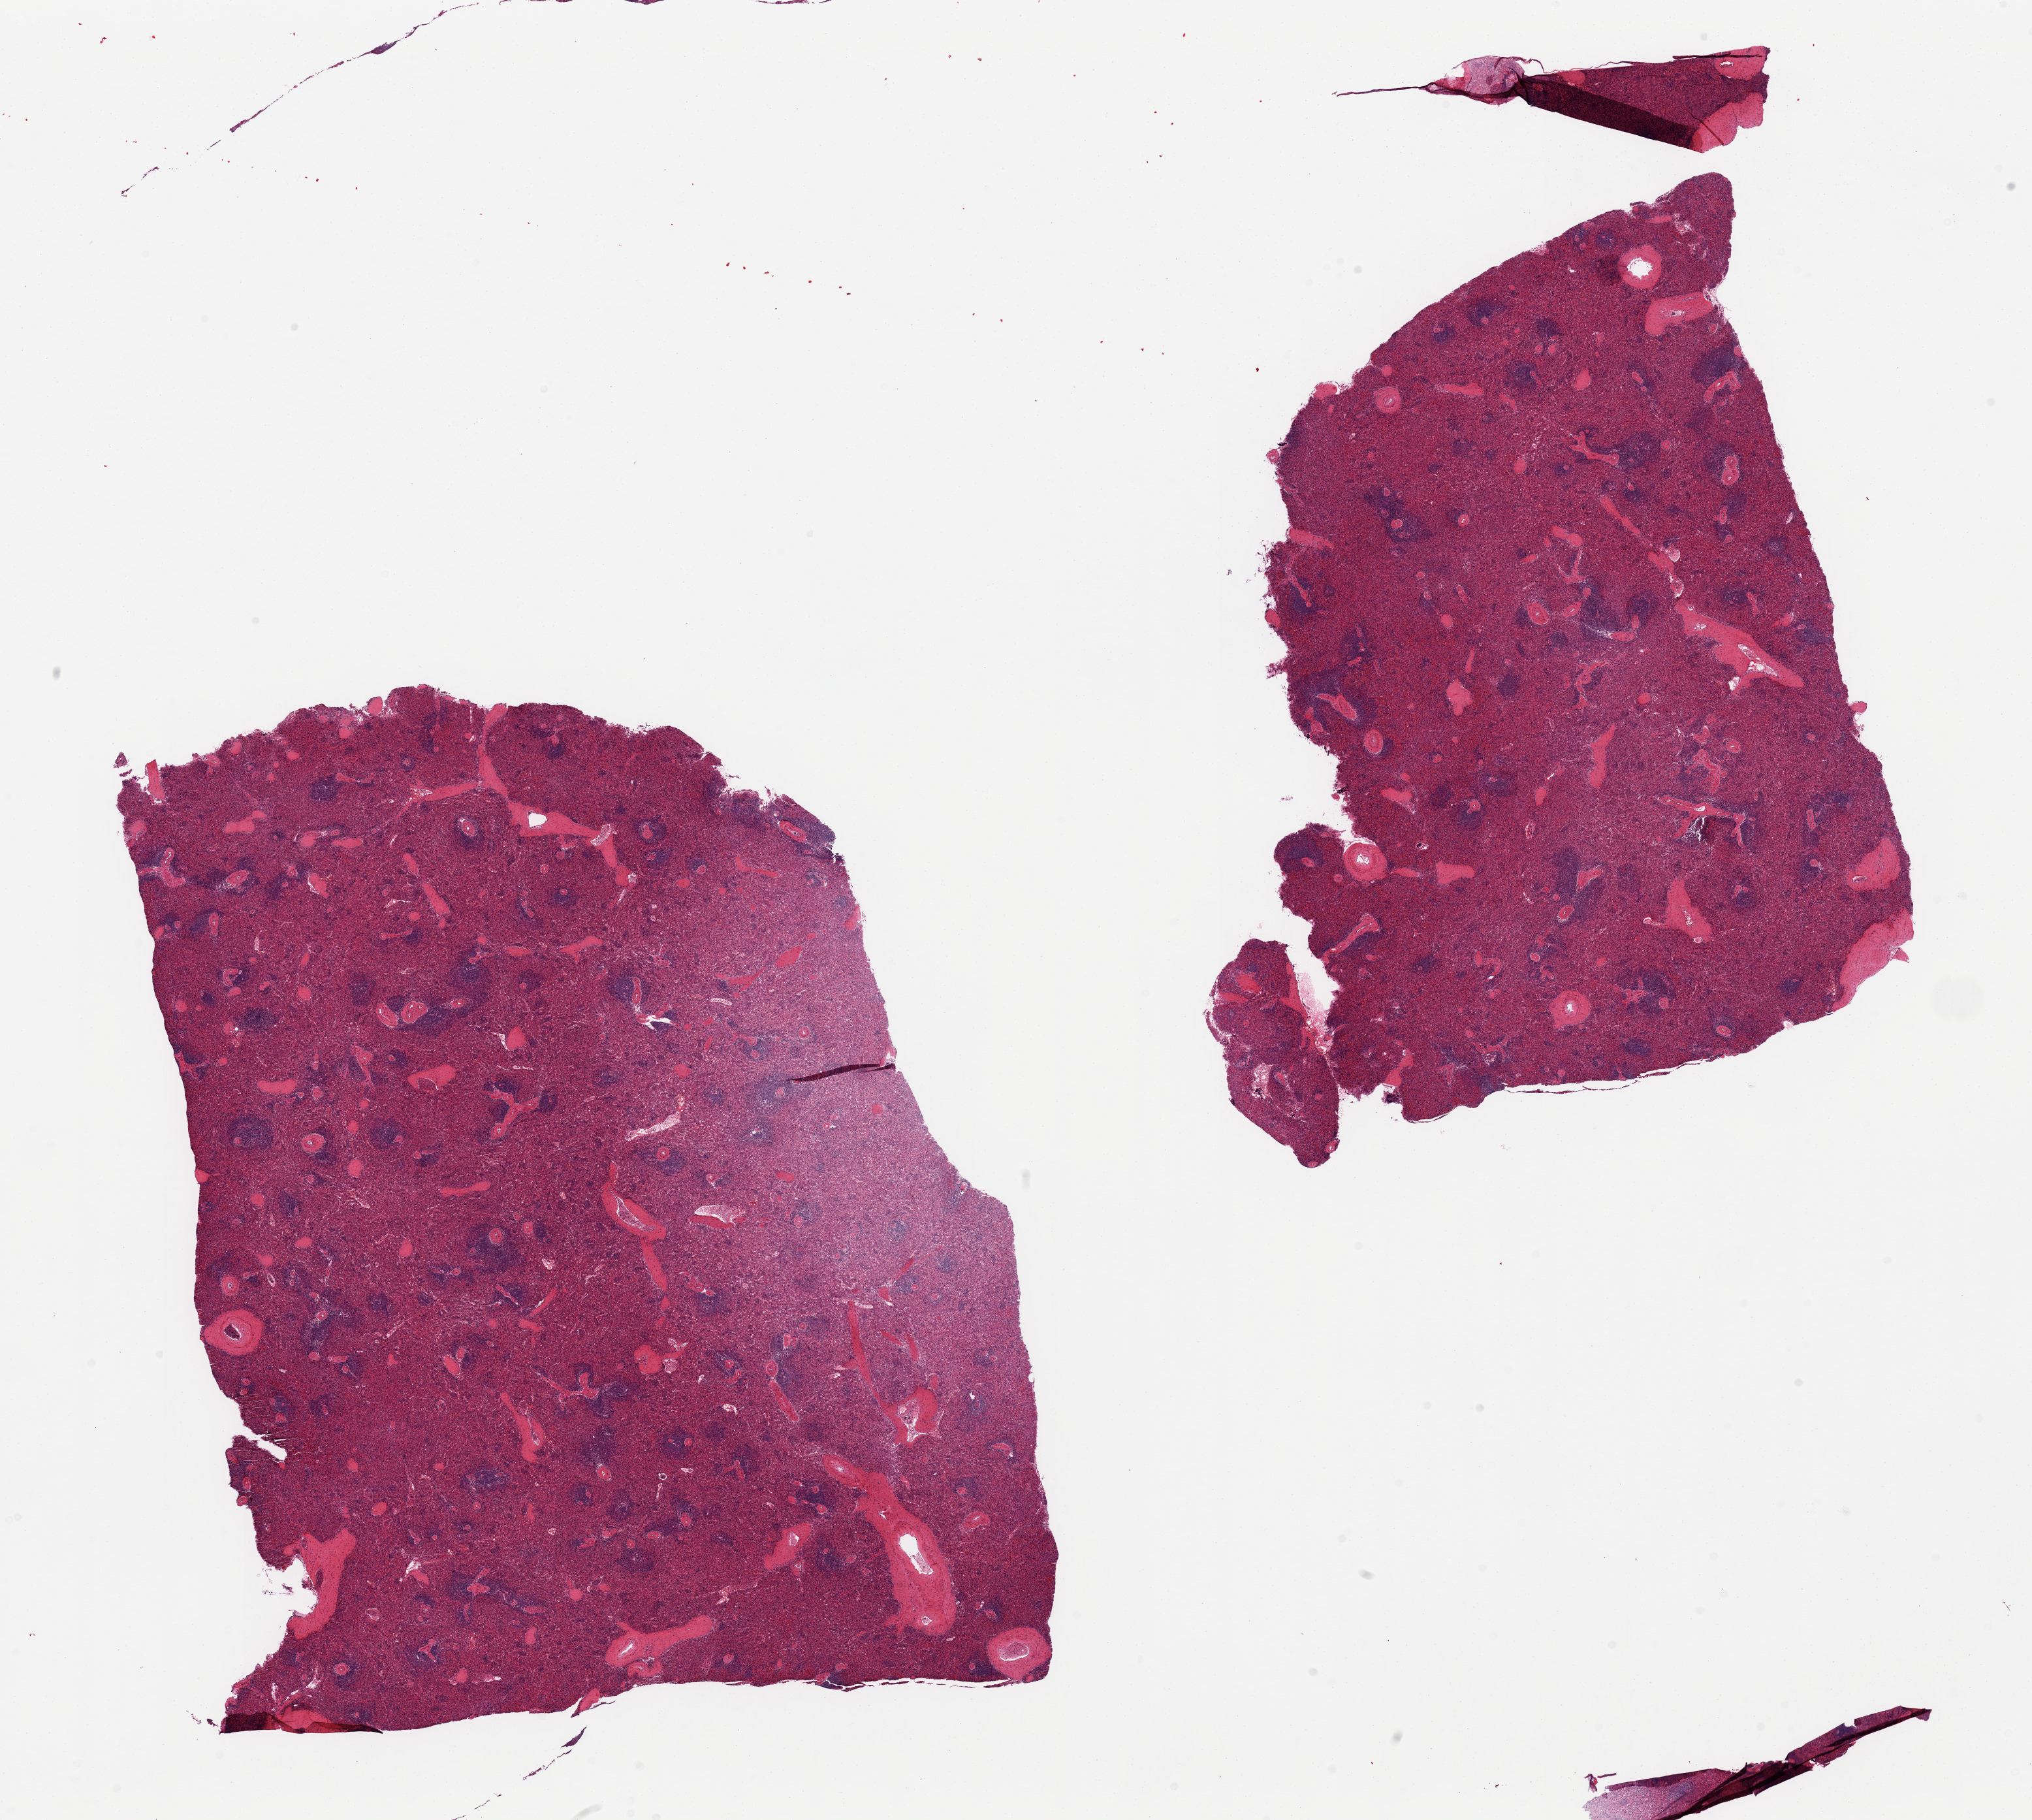
Whole-slide image, haematoxylin and eosin stain — shown as a low-resolution overview of the whole scanned area (about 24.6 x 22.0 mm, from a 20x scan), PAXgene-fixed, paraffin-embedded tissue, sampled site (target tissue): spleen, donor tissue sample. Donor sex: male.
* review note (as recorded): 2 pieces, moderate congestion